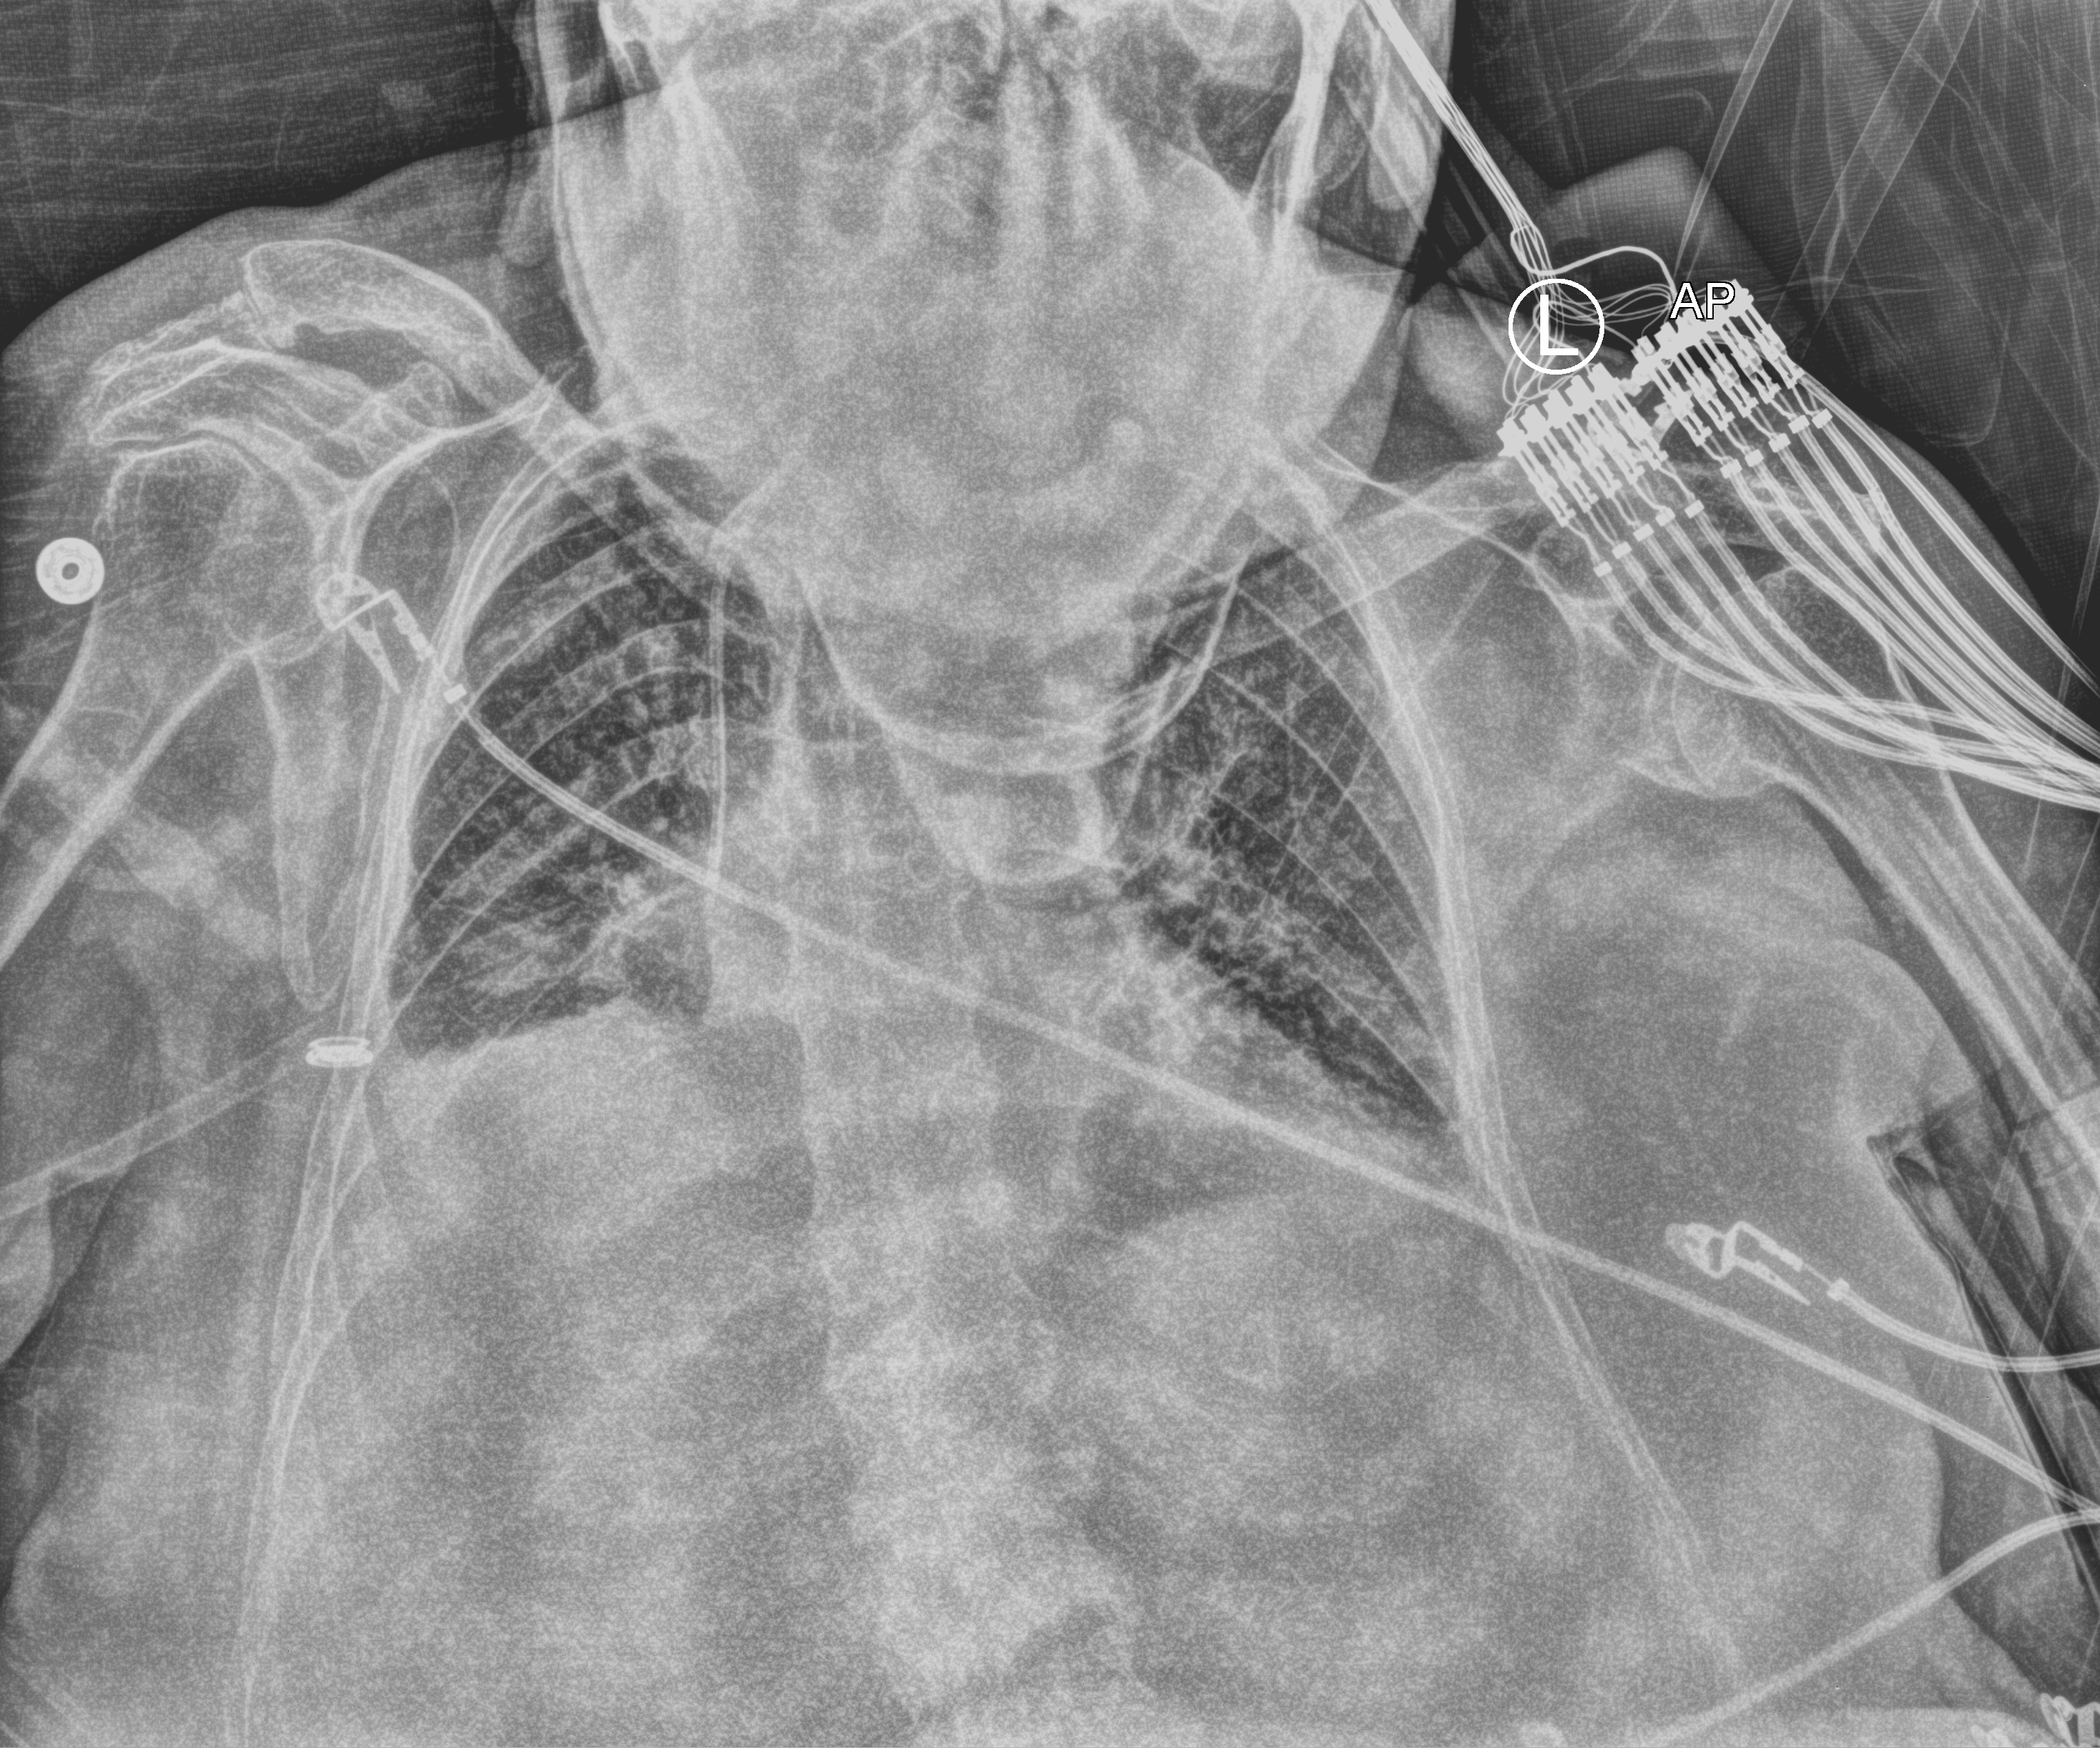
Bedside chest radiograph (computed radiography). Patient hospitalised with COVID-19; female, aged 75–90 years.
Admission-level facts for this patient (not findings on this image; timing relative to this image not recorded): other chronic lung disease (admission record): no; hypertension (admission record): yes; COPD (admission record): yes.